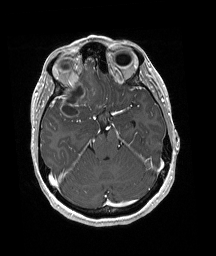
Brain MRI from a brain-tumour surgery series, one axial slice; position 123 of 192 along the scan axis; T1-weighted post-contrast; 1 mm slice thickness; 216 × 256 image matrix. From the clinical record (not read from this slice): histopathology: Oligodendroglioma; WHO grade: 3; IDH mutation: yes.
Structures marked on this image (outlined manually by an expert reader):
- tumour: bounding box (x1, y1, x2, y2) in pixels: (52, 74, 97, 118)